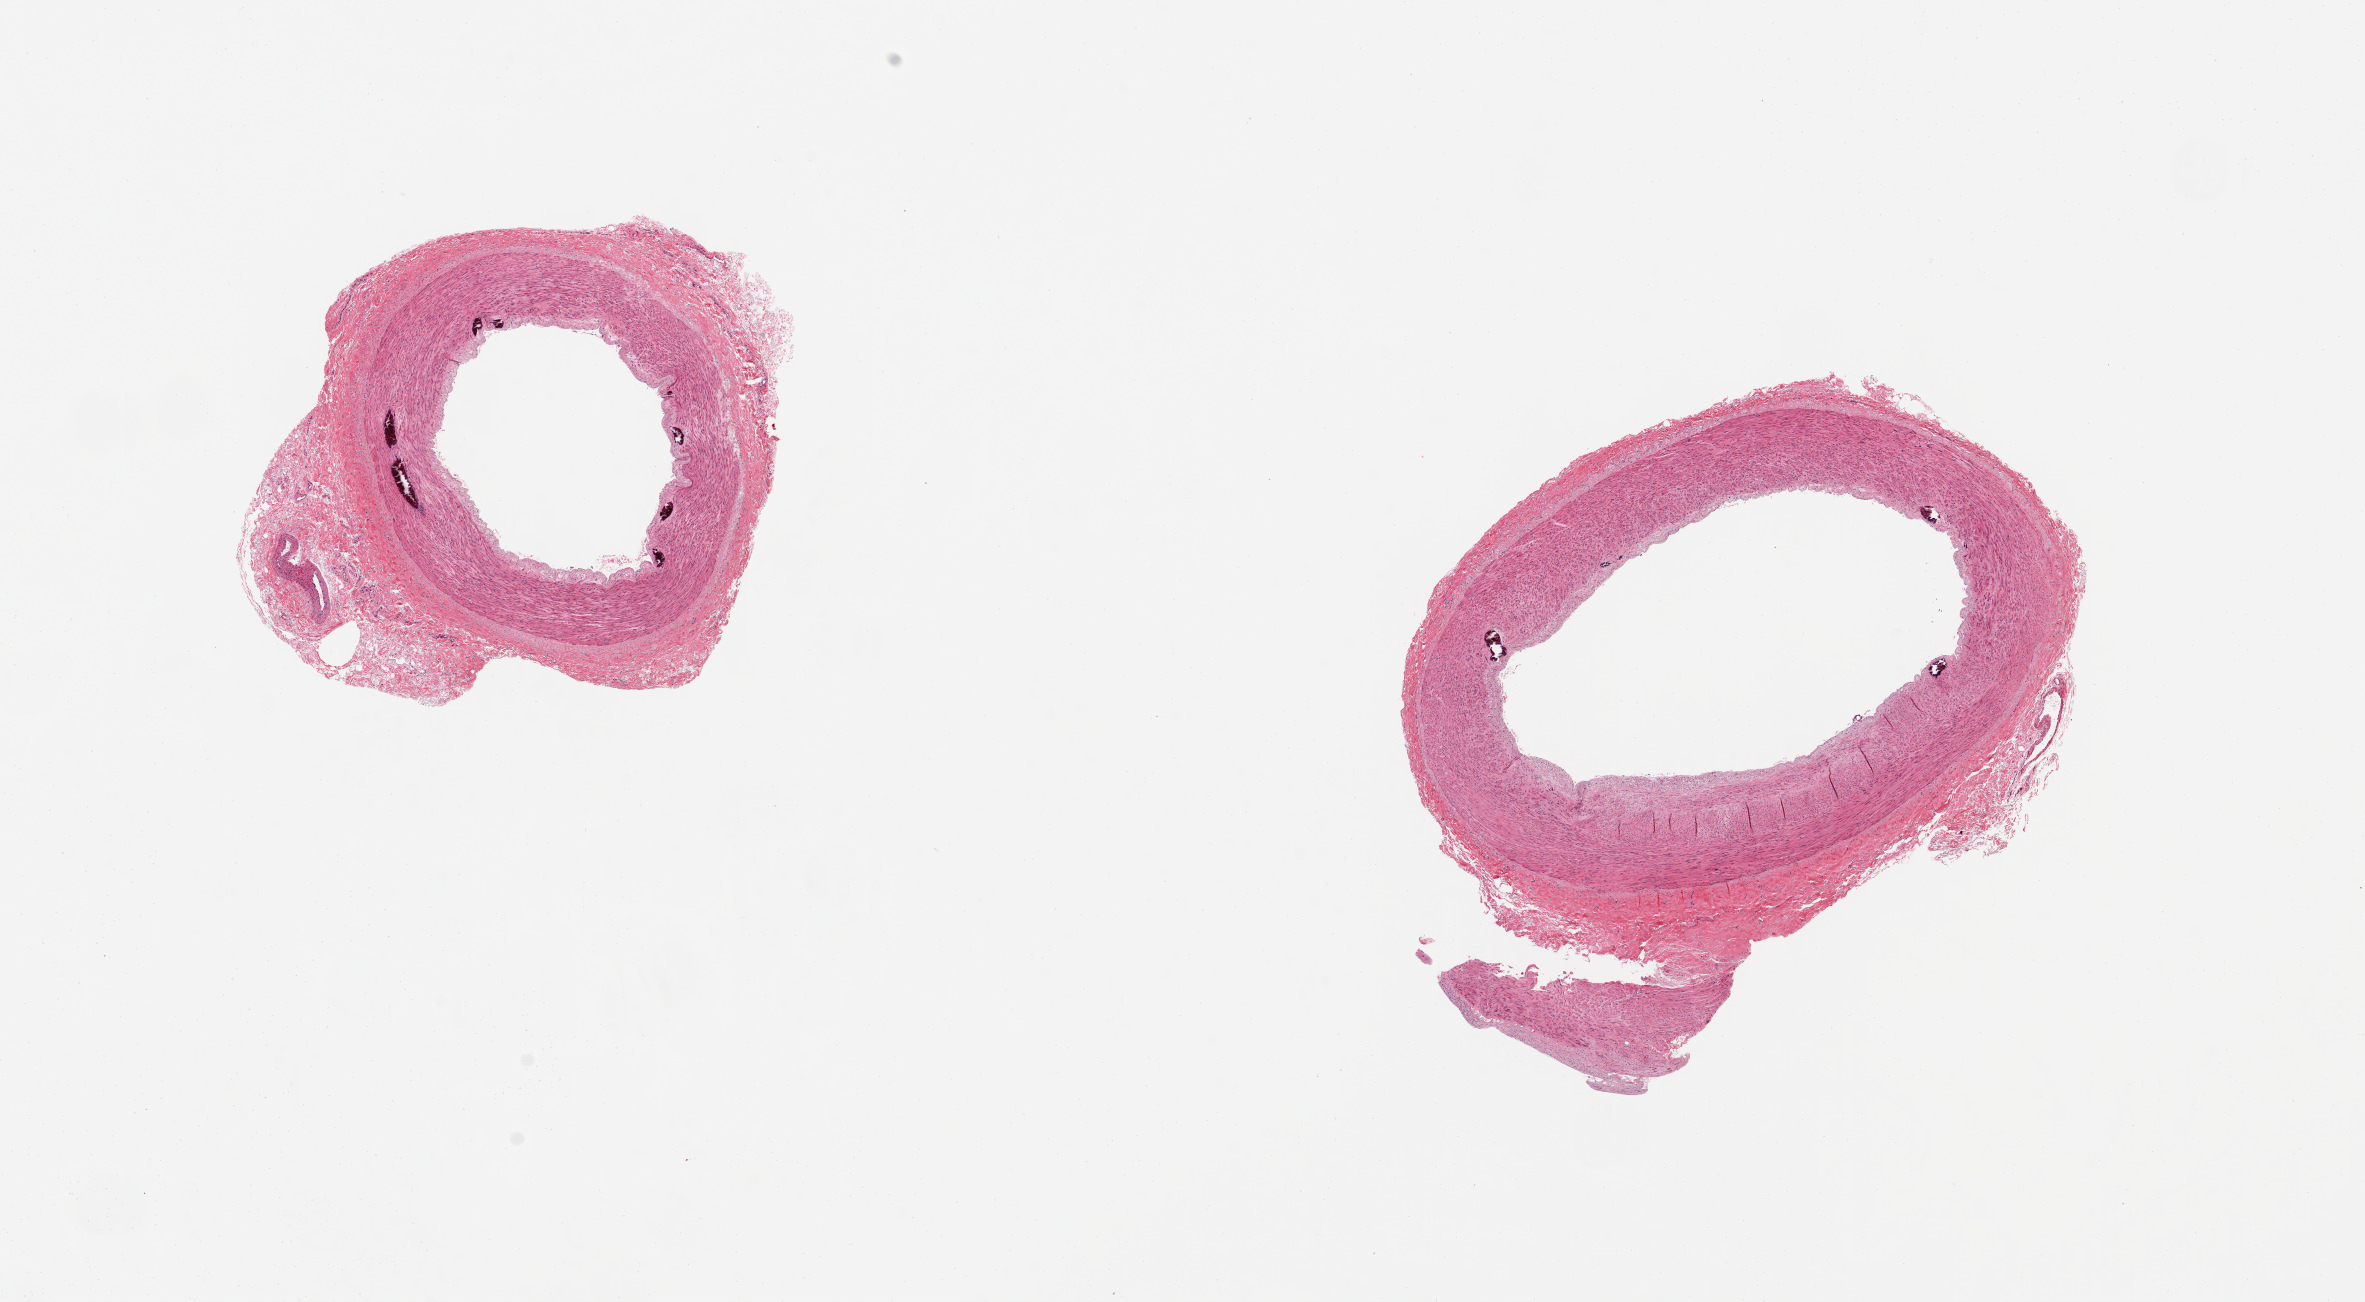
H&E whole-slide image, brightfield, shown as a low-resolution overview of the whole scanned area (about 18.7 x 10.3 mm); PAXgene-fixed, paraffin-embedded tissue; section of tibial artery (target tissue); donor tissue sample. Donor: female.
Pathologist's review note for this sample: 2 pieces, 5x4 & 6x5mm; clean specimens; Monckeberg's medial sclerosis in both.